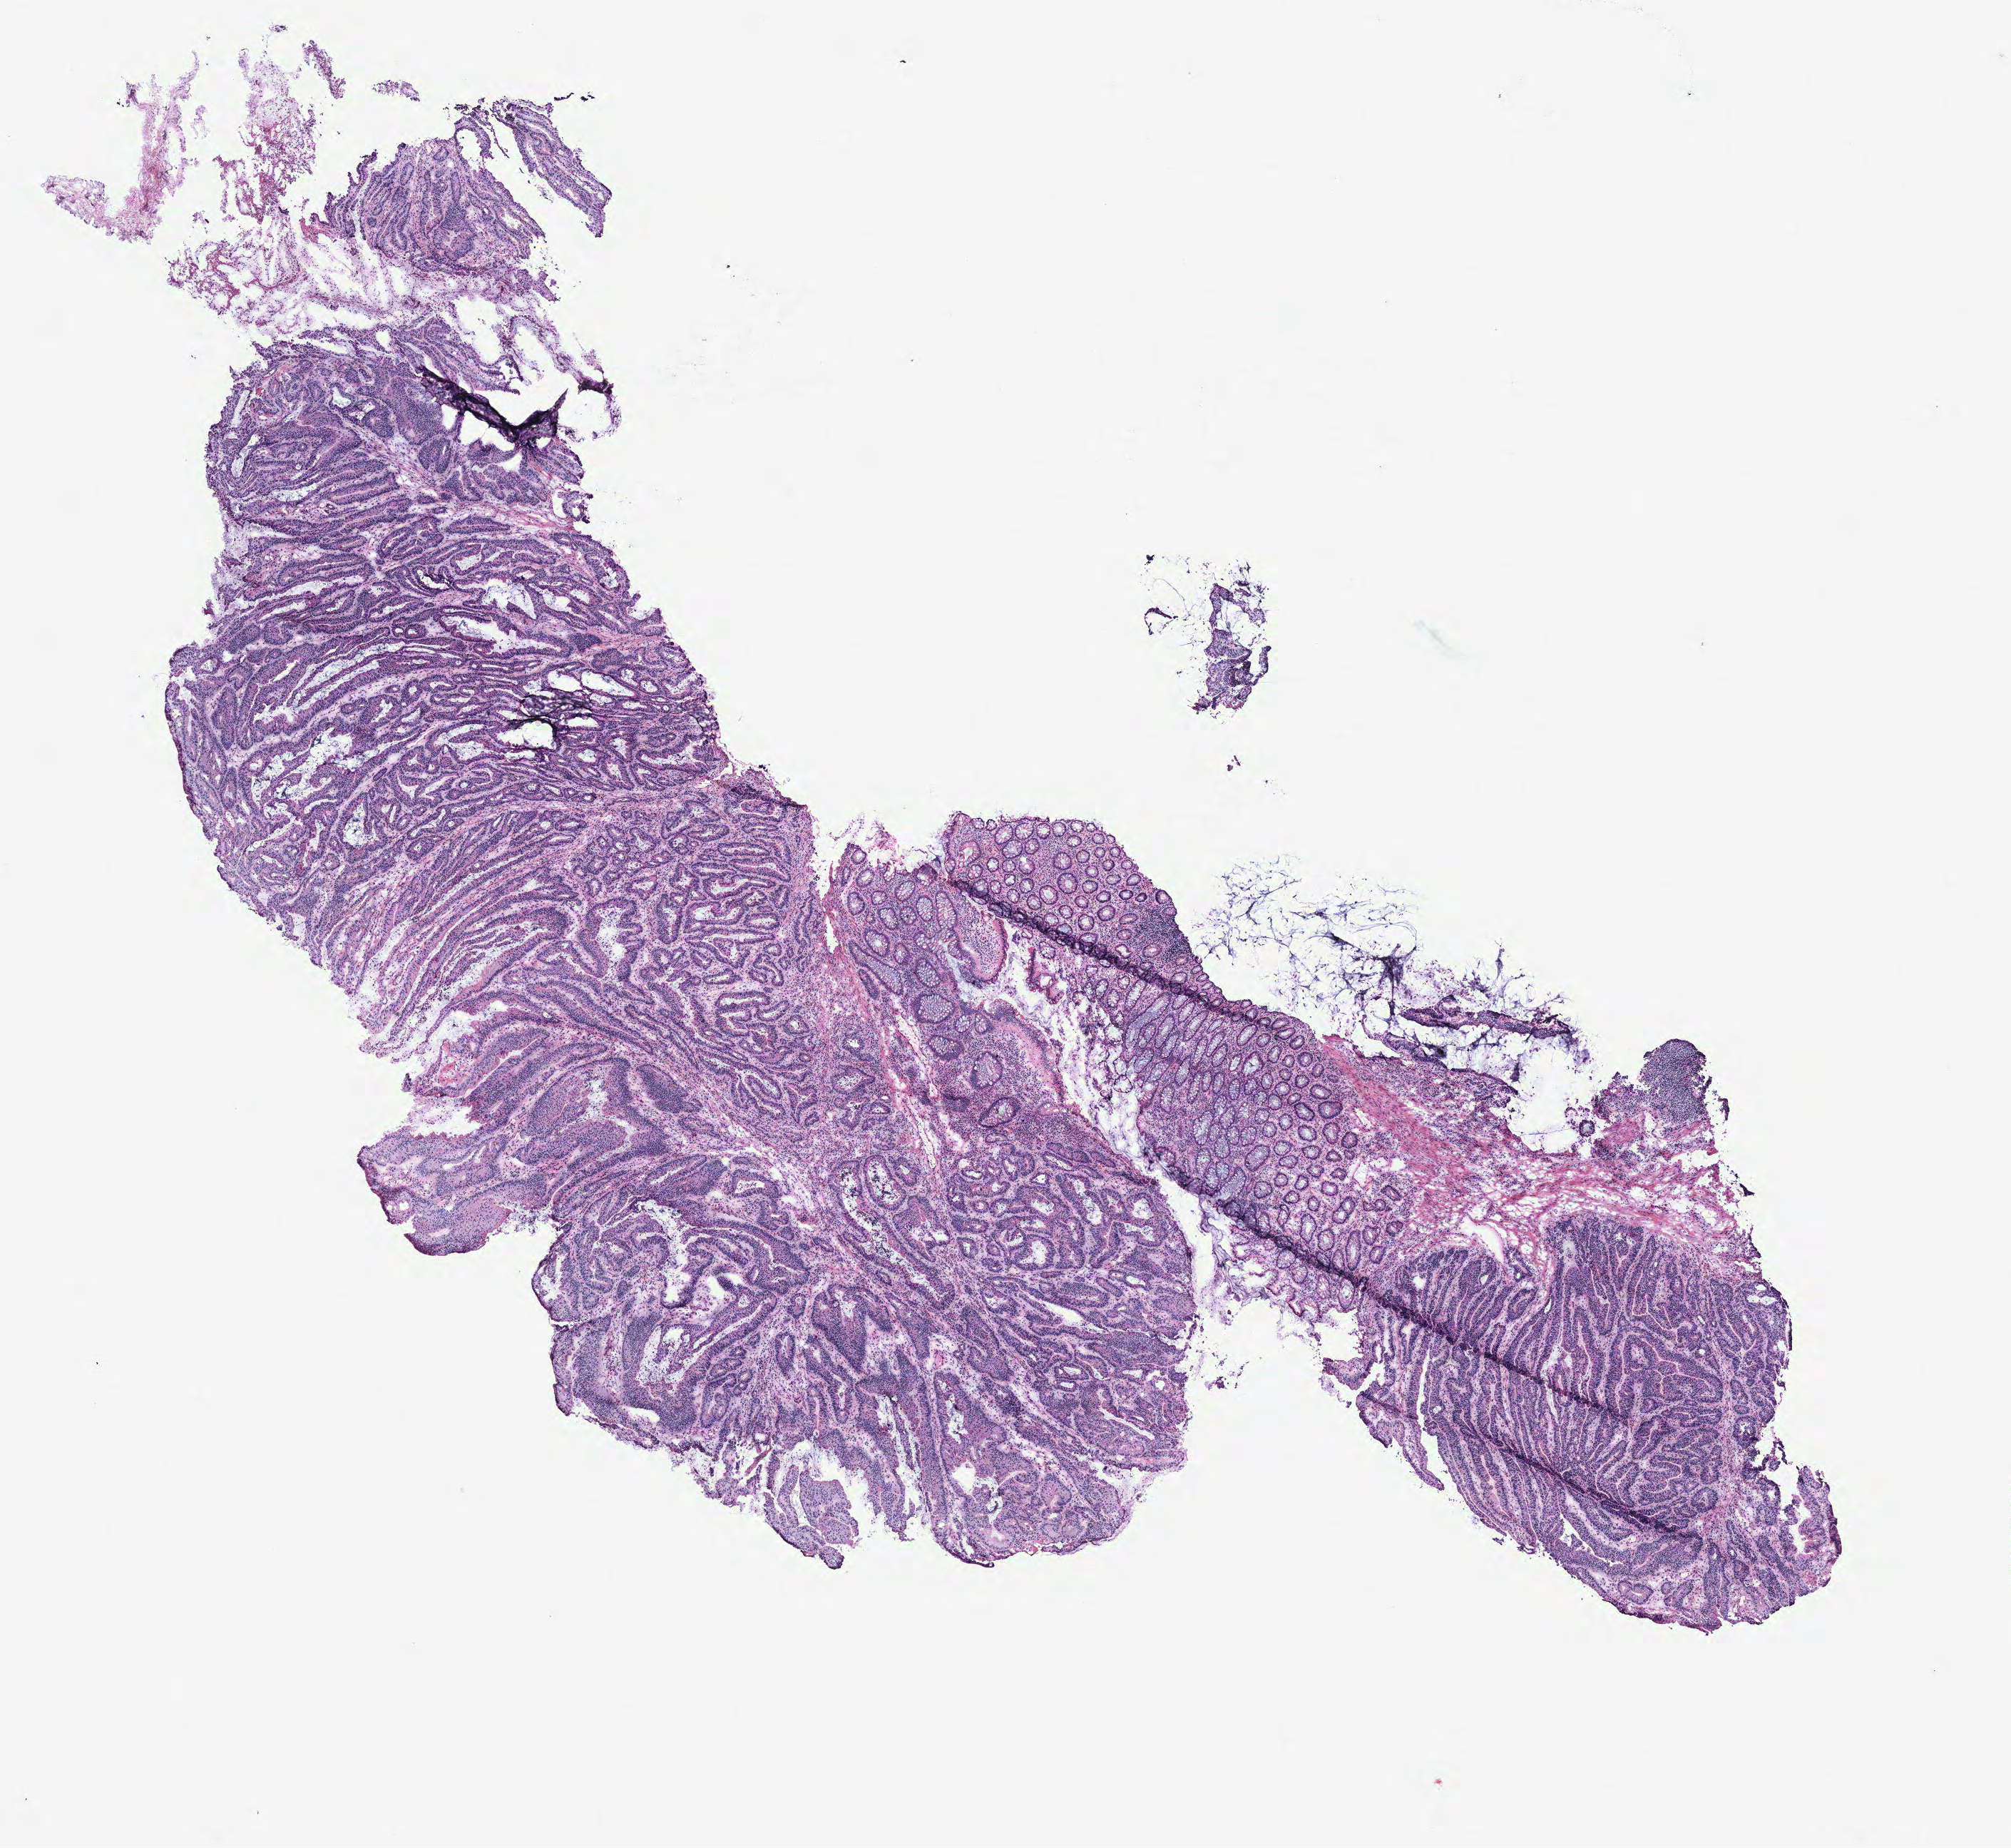
Digitized H&E-stained tissue section (whole slide), whole scanned area (about 11.3 x 10.4 mm) shown as a low-resolution overview; tumour tissue sample, colon. 73-year-old male patient.
AJCC pathologic stage: IIB. Primary tumour site (as recorded): colon. Diagnosis: Adenocarcinoma, NOS.